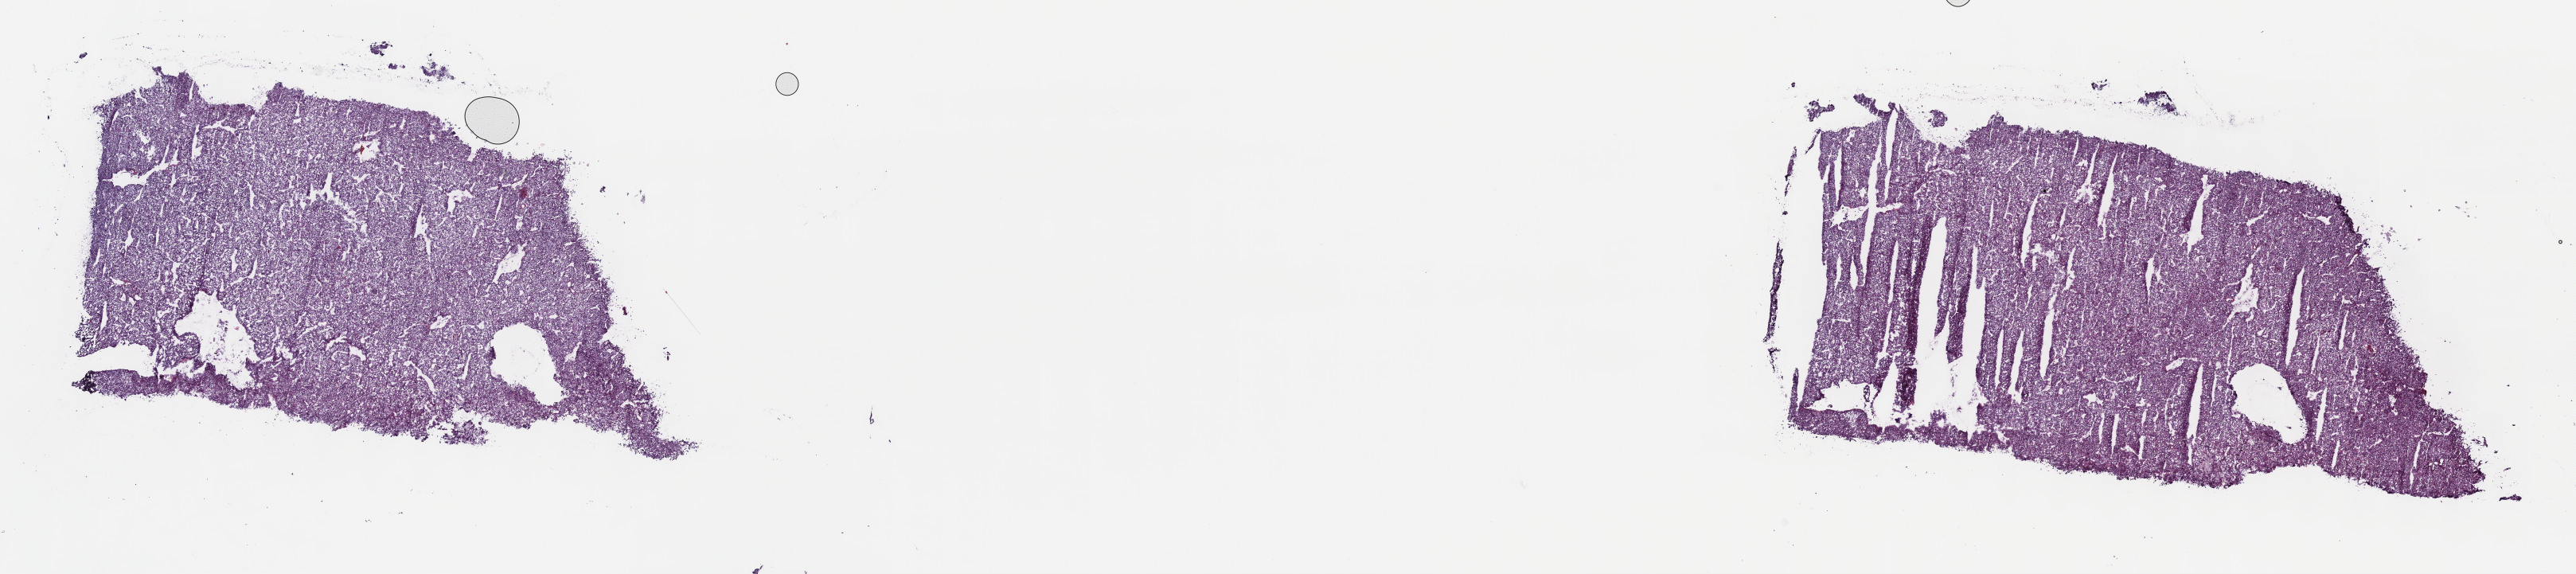
Hematoxylin and eosin (H&E) stained whole-slide image, whole scanned area (about 26.2 x 5.8 mm, acquisition: 40x scan) shown as a low-resolution overview, frozen section from the top of the tissue portion, liver, primary tumour sample. Patient: male, age at initial diagnosis 57 years. Histologic grade: G2 (moderately differentiated). Slide review estimates, as recorded: tumour cells 94%, tumour nuclei 95%, normal cells 0%, stromal cells 4%, necrosis 2%. Infiltration values recorded for this section: lymphocyte infiltration 4%, monocyte infiltration 1%, neutrophil infiltration 0%.
Diagnosis: Hepatocellular carcinoma, NOS. AJCC pathologic stage: IIIA (6th edition).